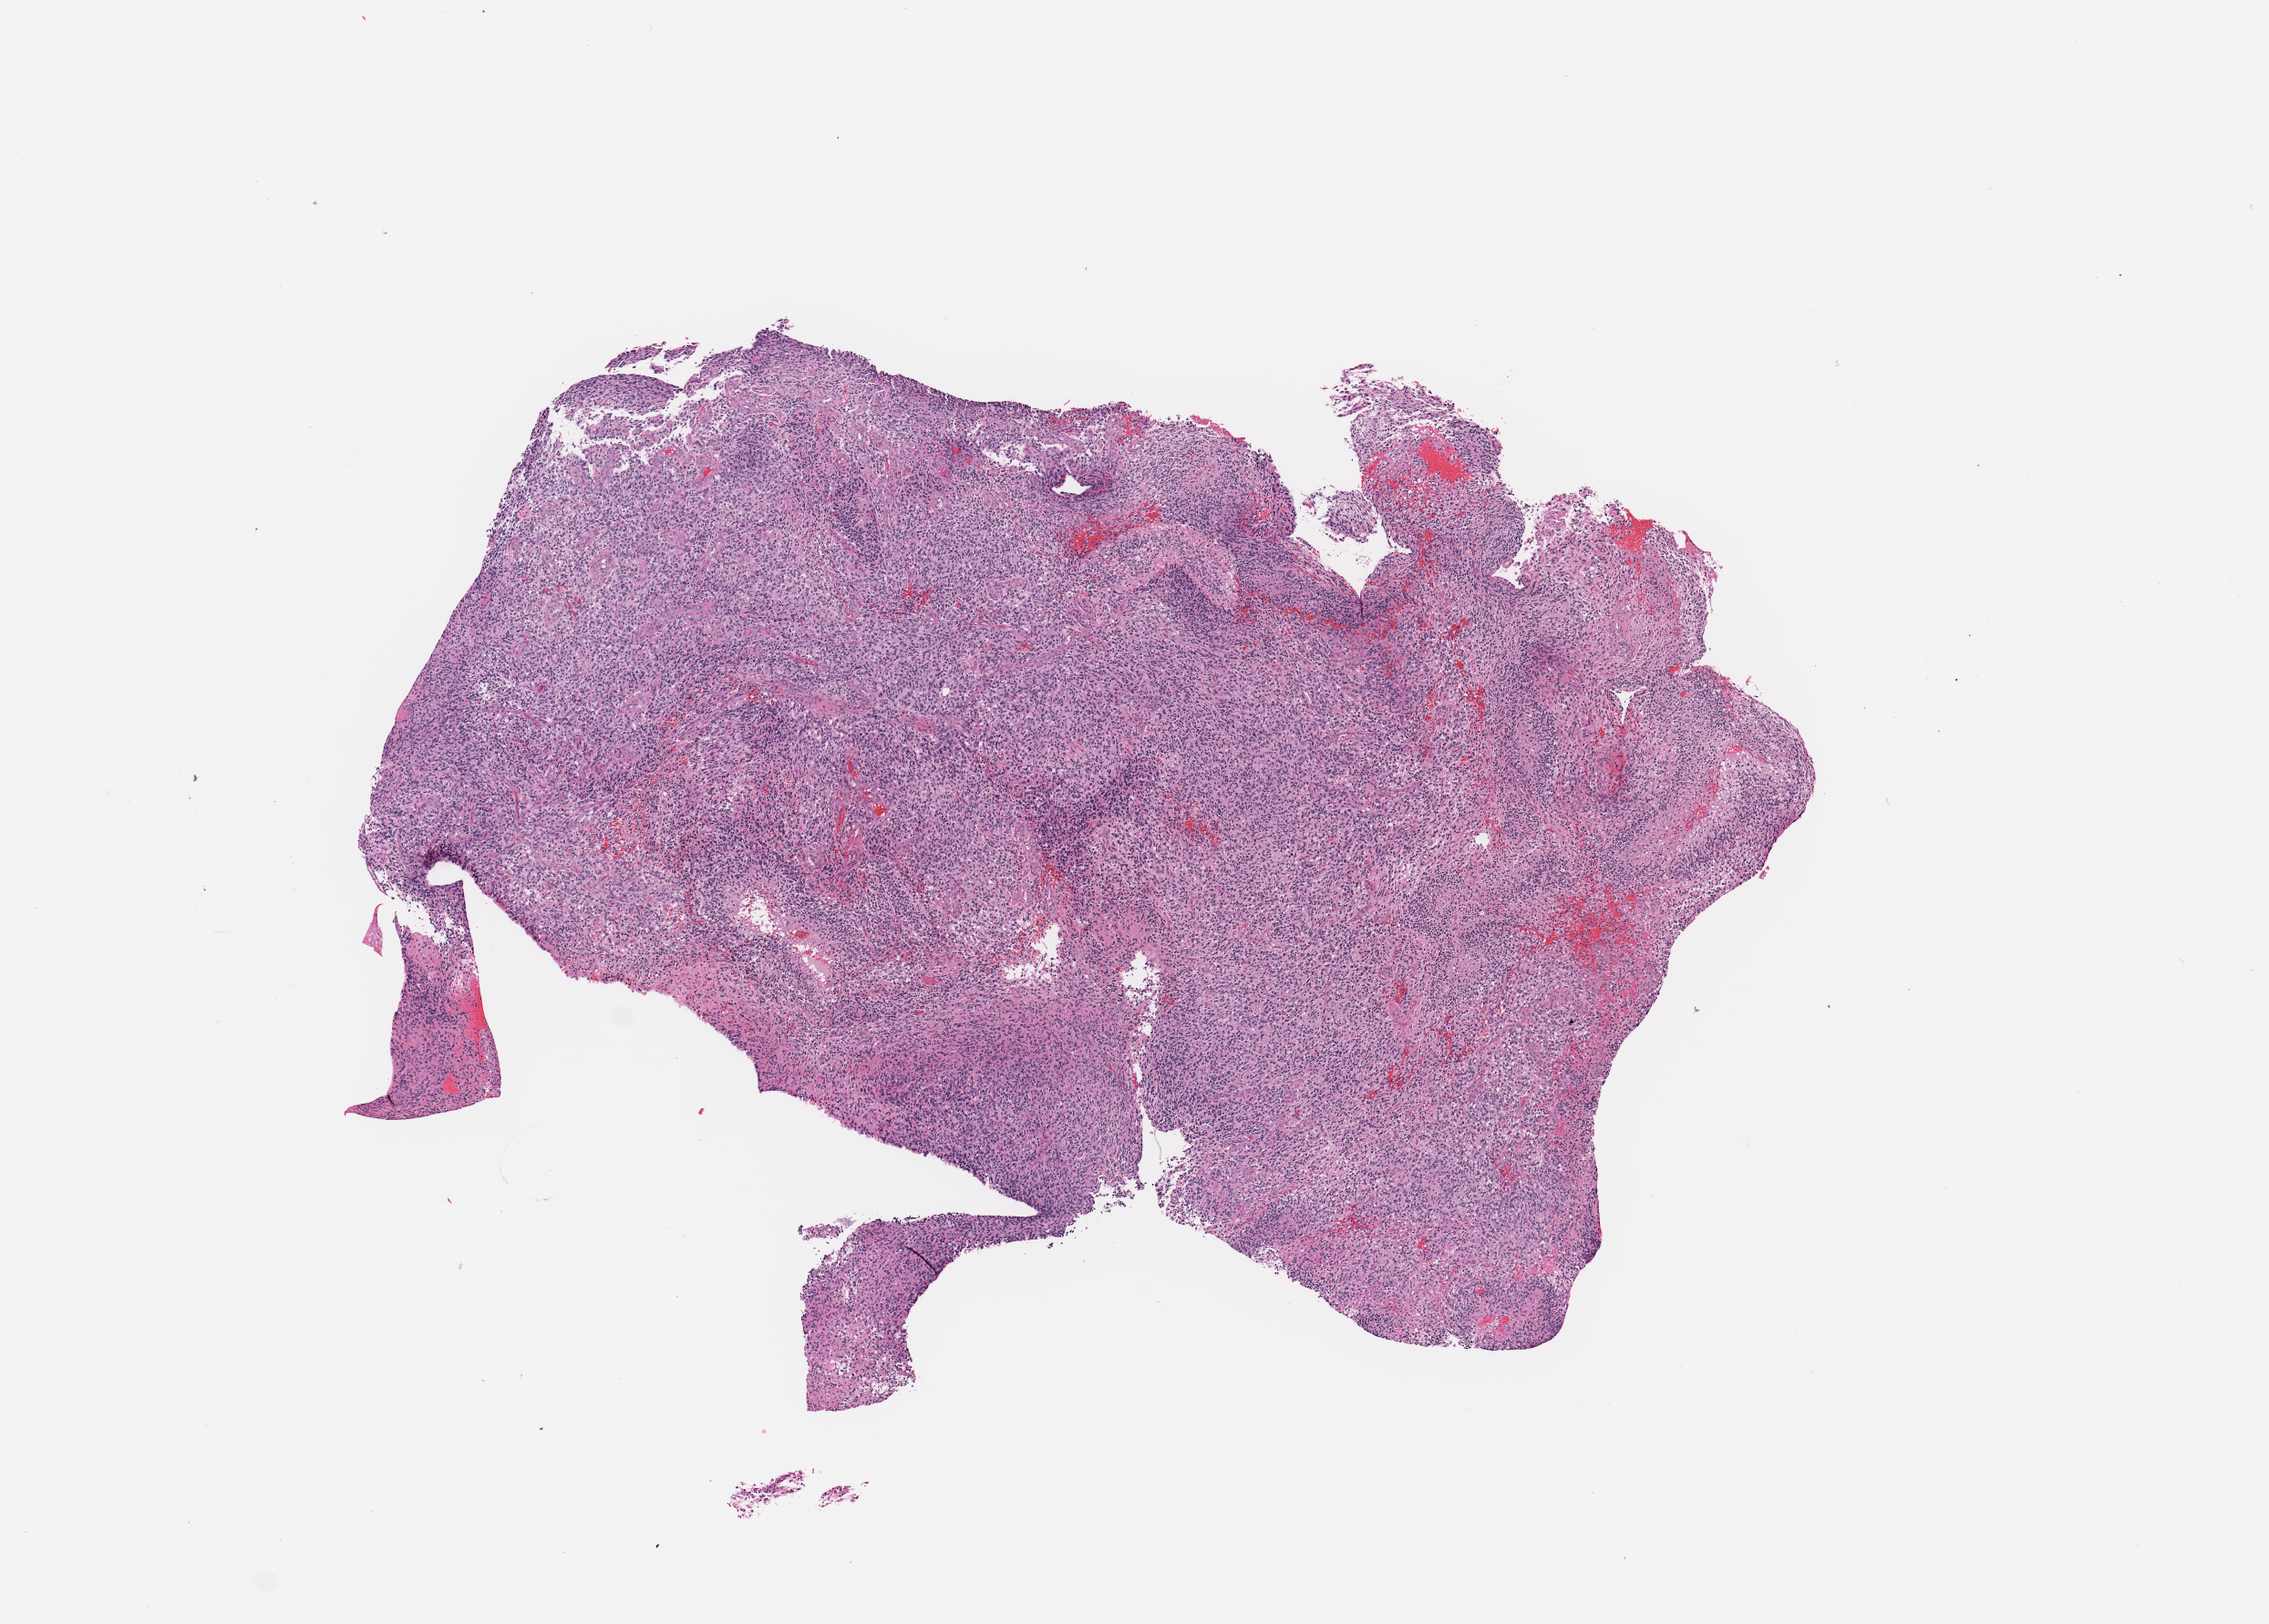
Whole-slide histology image, Hematoxylin and eosin (H&E) stained, a low-resolution overview of the entire scanned area, about 9.8 x 7.0 mm. Tumour tissue sample, sampled site: brain. Patient: male, age 66 years. Slide review estimates, as recorded: tumour nuclei 85%, necrosis 5%.
- diagnosis: Glioblastoma